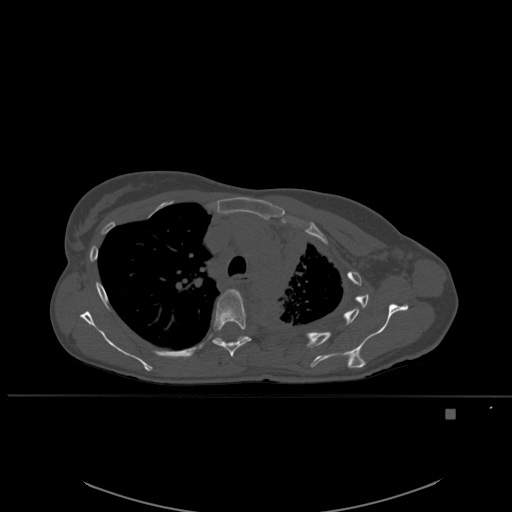
CT including the spine, one axial slice. Position 398 of 537 along the scan axis. Bone window (W 1800 / L 400 HU). 512 × 512 image matrix. Patient: female, 45 years. Case-level facts recorded for this patient, not image findings: primary cancer: lung.
Outlined on this slice (semi-automatically segmented with operator editing):
- T5 vertebra: box from (x=212, y=289) to (x=252, y=357) px
- T6 vertebra: (x=214, y=336)–(x=244, y=342)